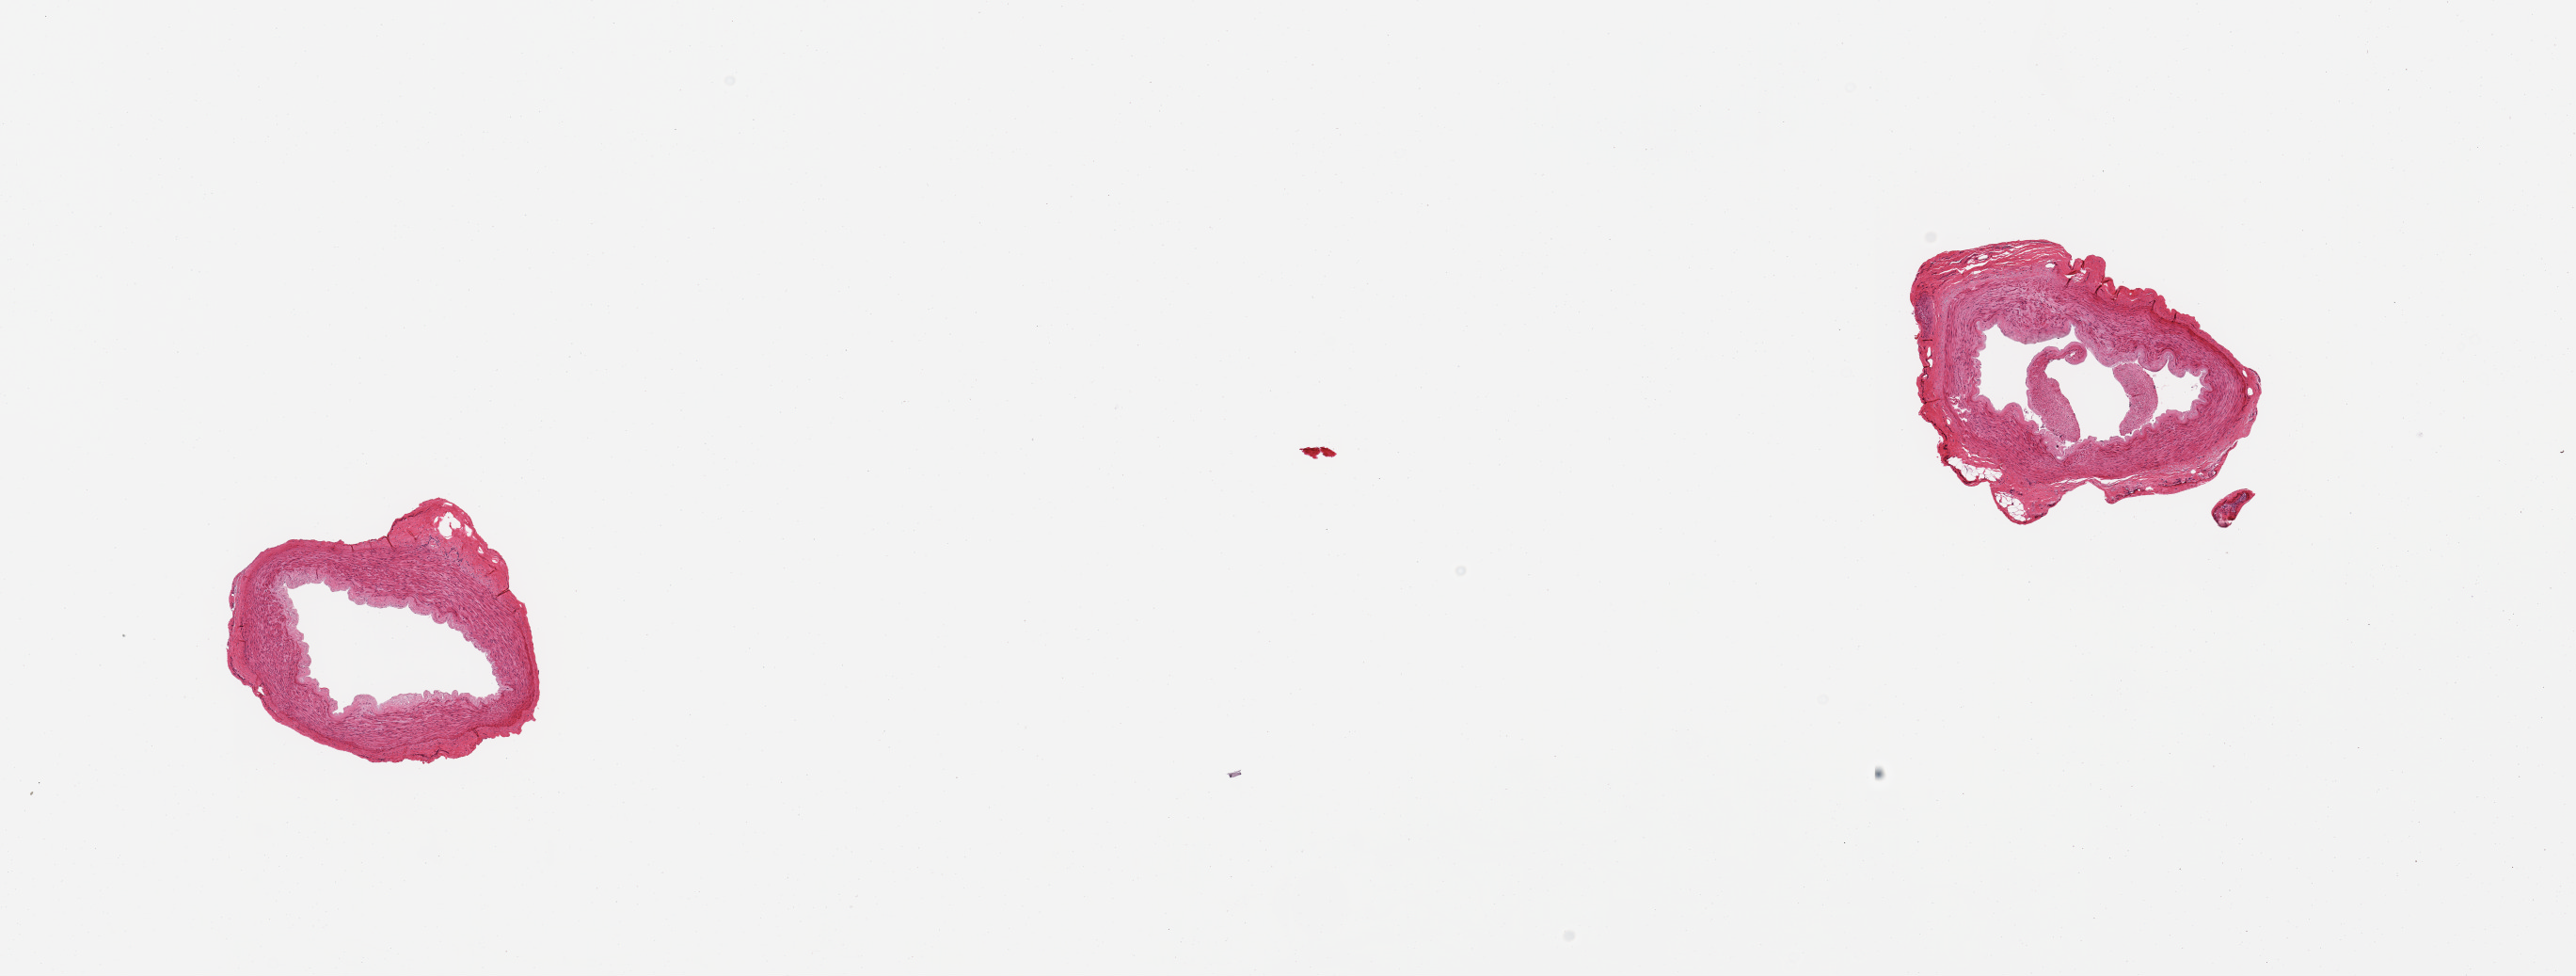
Haematoxylin and eosin whole-slide image — shown as a low-resolution overview of the whole scanned area (about 21.7 x 8.2 mm, from a 20x scan); PAXgene-fixed, paraffin-embedded tissue; sampled site (target tissue): tibial artery; donor tissue sample. Donor sex: male.
- reviewer comment on this tissue sample: 2 pieces: slight plaque well trimmed